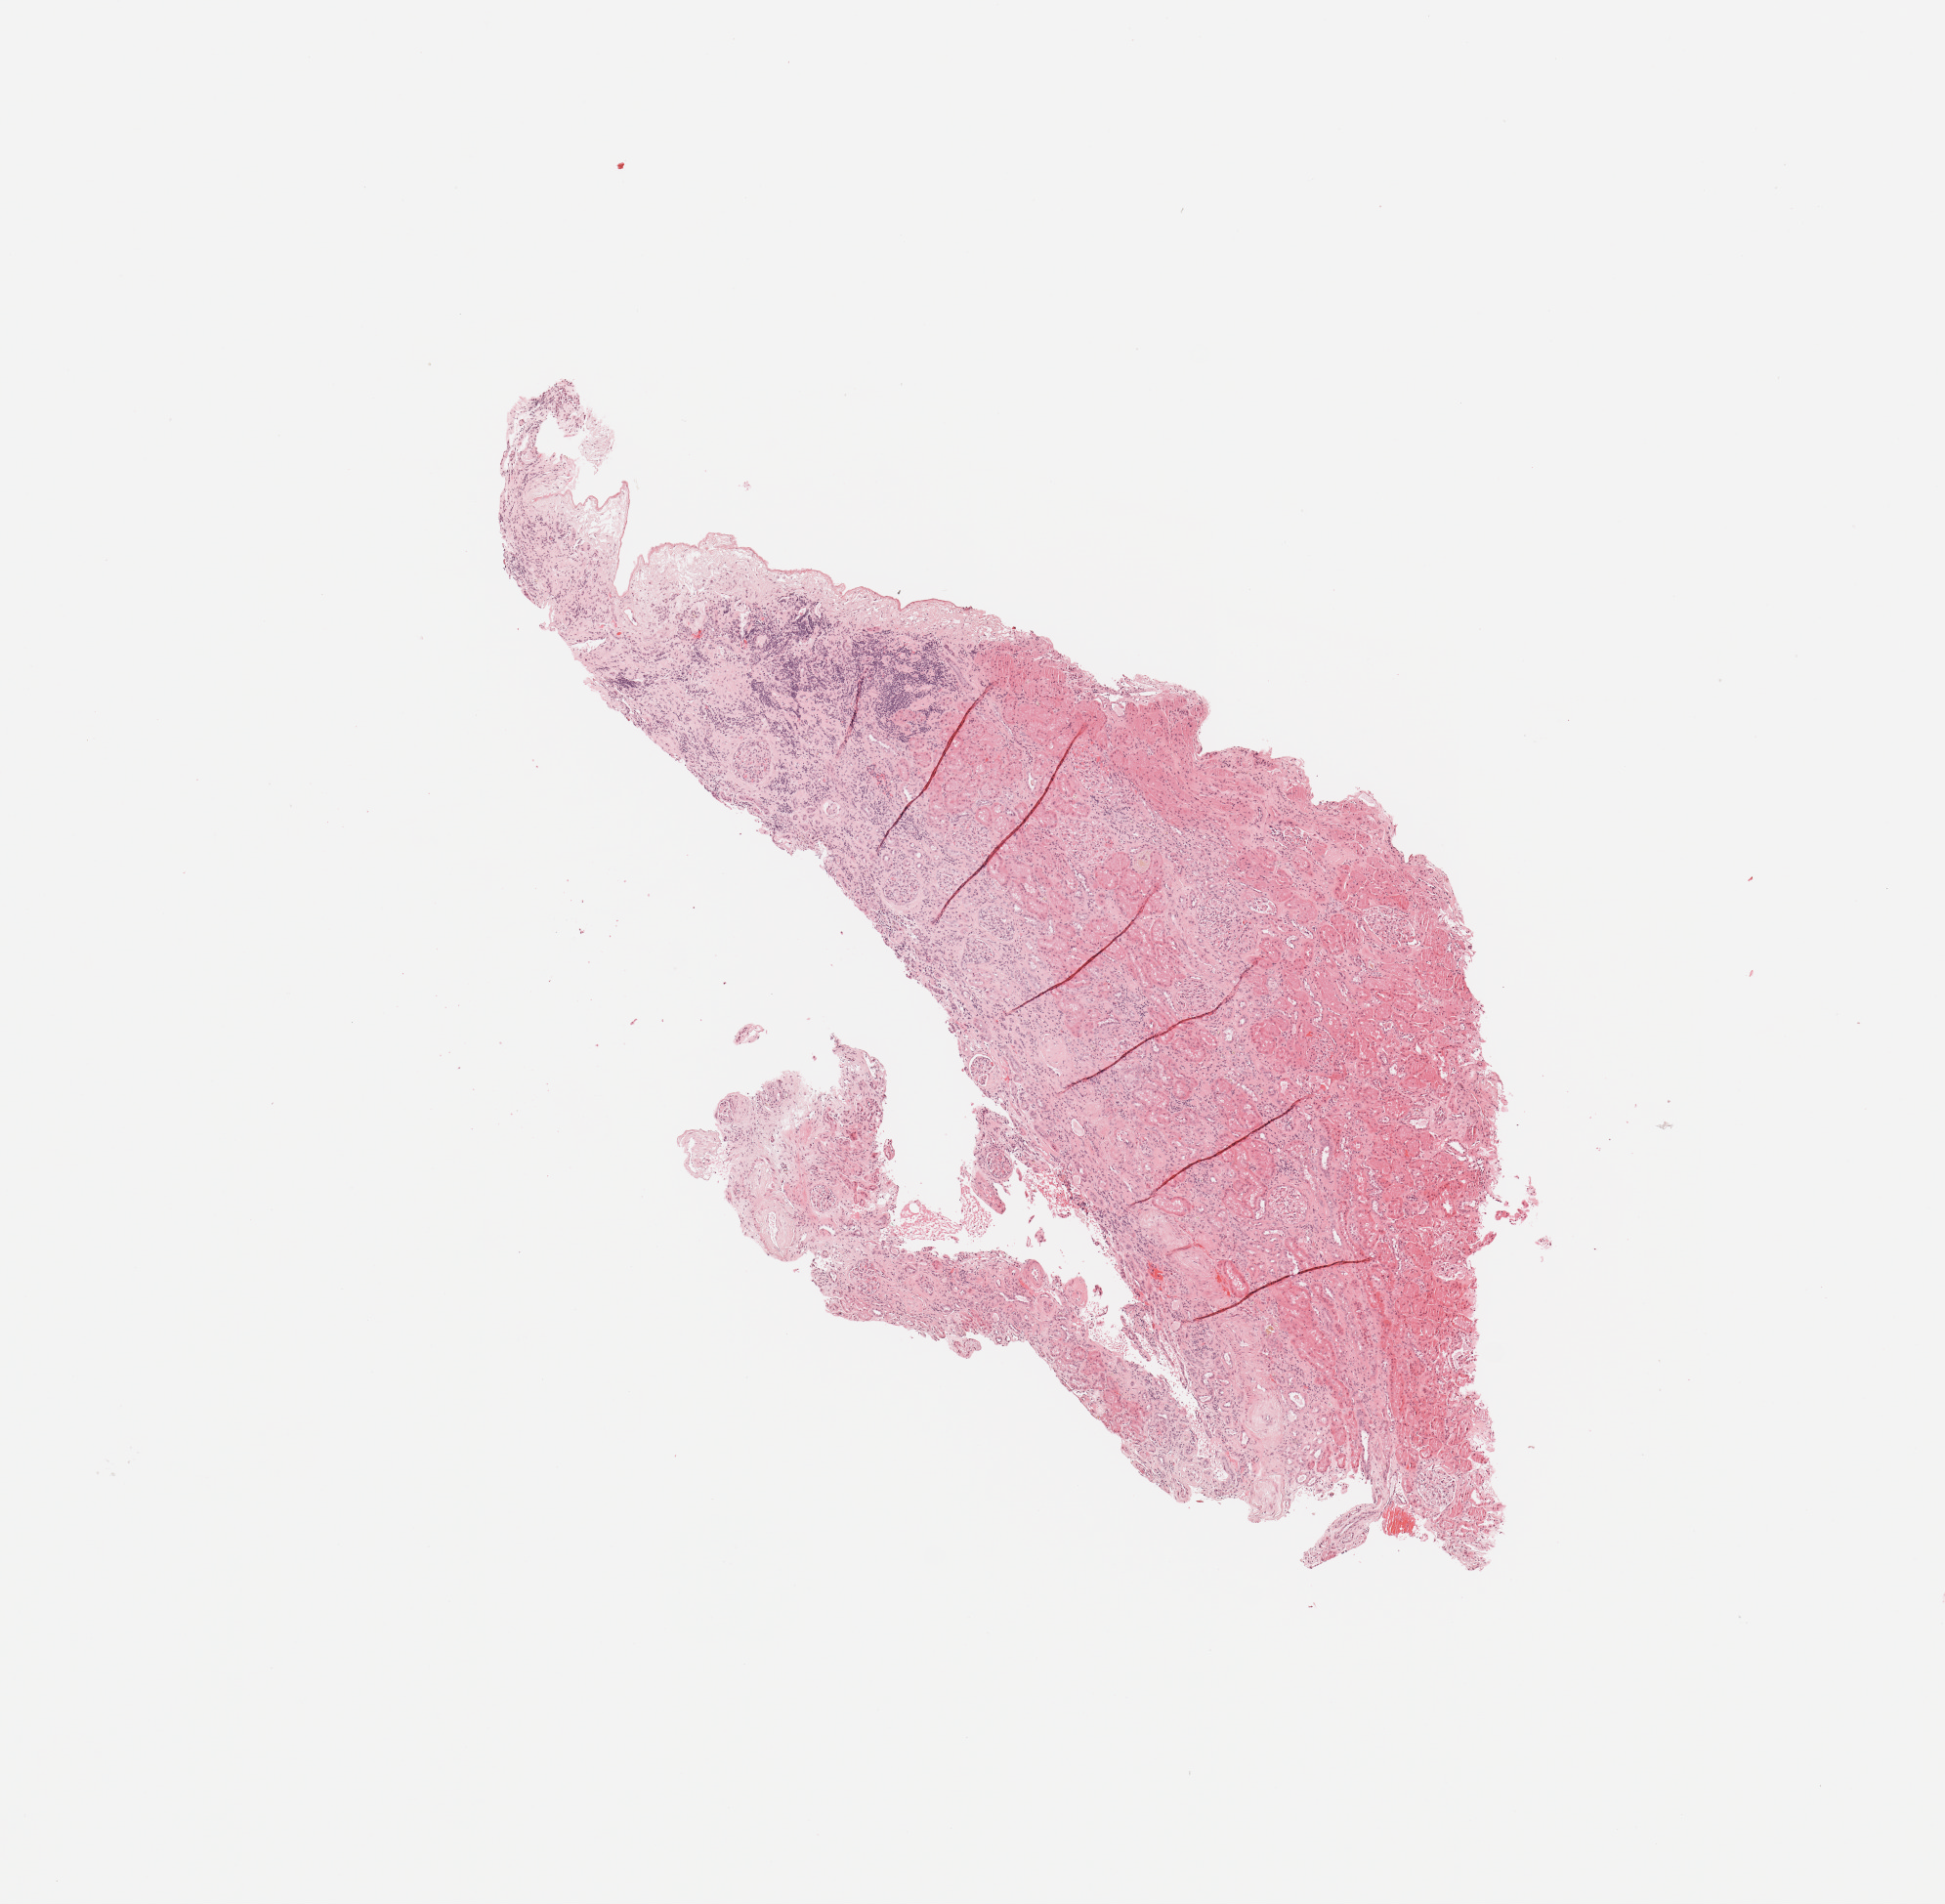
H&E-stained whole-slide image — low-resolution overview of the scanned area, about 7.9 x 7.7 mm (slide scanned at 20x); normal (non-tumour) tissue sample, sampled site: kidney. 83-year-old male patient.
- this section: normal (non-tumour) tissue from the same patient
- patient diagnosis: Renal cell carcinoma, NOS